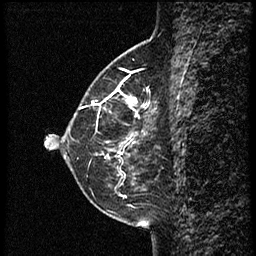
Breast MRI (dynamic contrast-enhanced), one sagittal slice; position 21 of 60 along the scan axis; dynamic contrast-enhanced study with each time point stored as its own series, time point 2 of 3 at this slice position (early post-contrast, ordered by acquisition time); 1.5 T; TE 4.2 ms, TR 18.9 ms; 256 × 256 image matrix. Female patient. From the clinical record (not read from this slice): setting: breast cancer imaged before/during neoadjuvant chemotherapy; receptor status: HER2-positive.
Annotated regions visible in this slice (semi-automatic segmentation, software-assisted and operator-edited):
- analysis volume of interest (the breast-tissue region the enhancement analysis was run in; not a lesion): bounding box <77,70,161,147> (left, top, right, bottom; pixels)
- tumour enhancement mask (voxels above the 100 % enhancement threshold inside the analysis volume of interest): <93,97,139,137>